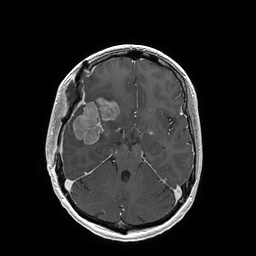
Brain MRI from a brain-tumour surgery series, one axial slice; position 107 of 202 along the scan axis; T1-weighted post-contrast; 1 mm slice thickness; 256 × 256 image matrix, field of view 250 × 250 mm. Case-level facts recorded for this patient, not image findings: histopathology: Glioblastoma; WHO grade: 4; IDH mutation: no; tumour location: Right Insular.
Annotated regions visible in this slice (expert manual segmentation):
- tumour: box from (x=73, y=98) to (x=119, y=145) px